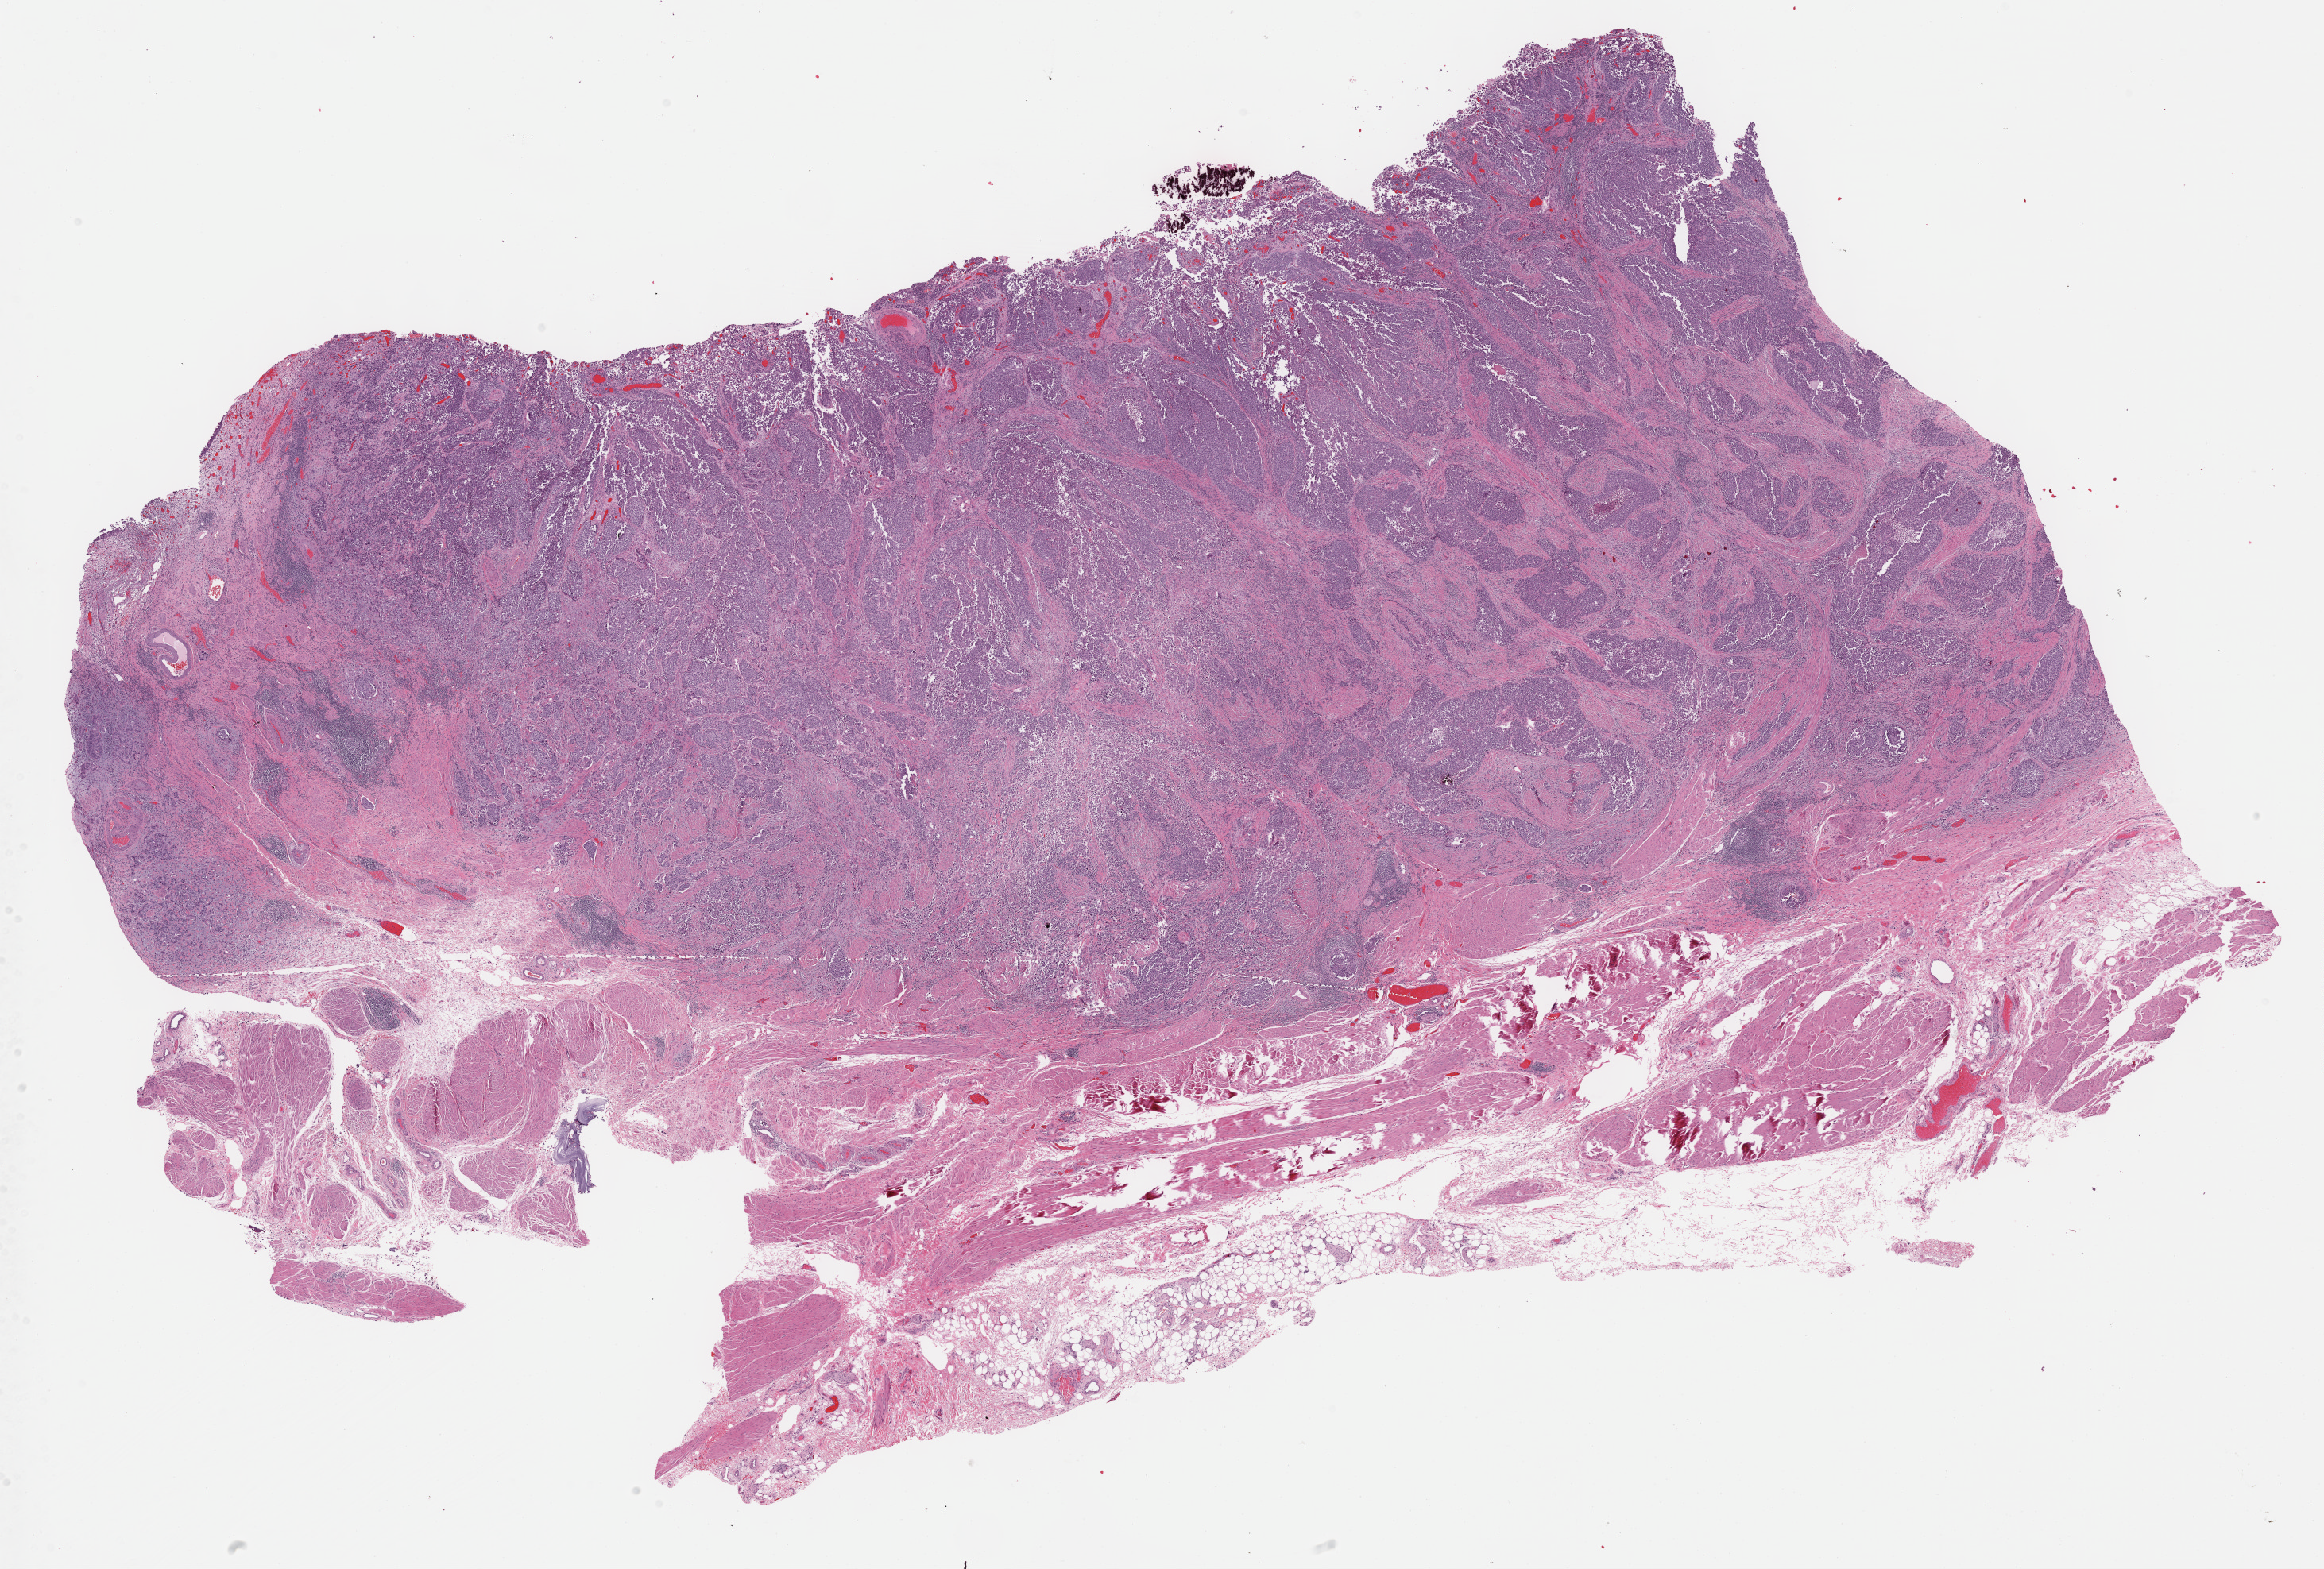
Whole-slide histology image, H&E-stained — shown as a low-resolution overview of the whole scanned area (about 23.7 x 16.0 mm), formalin-fixed paraffin-embedded (FFPE) diagnostic section, bladder, primary tumour sample. Female patient; age at initial diagnosis 67 years. Histologic grade: high grade.
Lymph nodes positive (case pathology): 2 of 24 examined. Pathologic diagnosis: Transitional cell carcinoma. AJCC pathologic stage: IV (6th edition). TNM: T3 N2 M0.